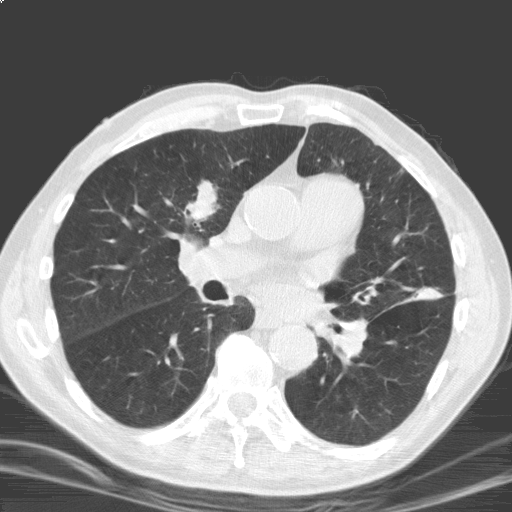
Low-dose screening chest CT, axial slice; second annual screen; lung window (W 1500 / L -600 HU); 3.2 mm slice thickness; standard (soft-tissue) reconstruction kernel (C); slice 86 of 184 in the series; 512 × 512 image matrix. Male, age 69 years at enrolment. Current smoker at enrolment.
Lesion marked by an expert reader, bounding box <173,174,231,230> (left, top, right, bottom; pixels). The screening reader recorded 2 non-calcified nodules or masses ≥4 mm on this exam; which of them this box marks is not recorded. Official screen result: positive, other. Lung cancer was diagnosed 17 days after this screen: squamous cell carcinoma, NOS, right upper lobe, moderately differentiated (G2), stage IB (AJCC 6th edition), 40 mm at pathology.